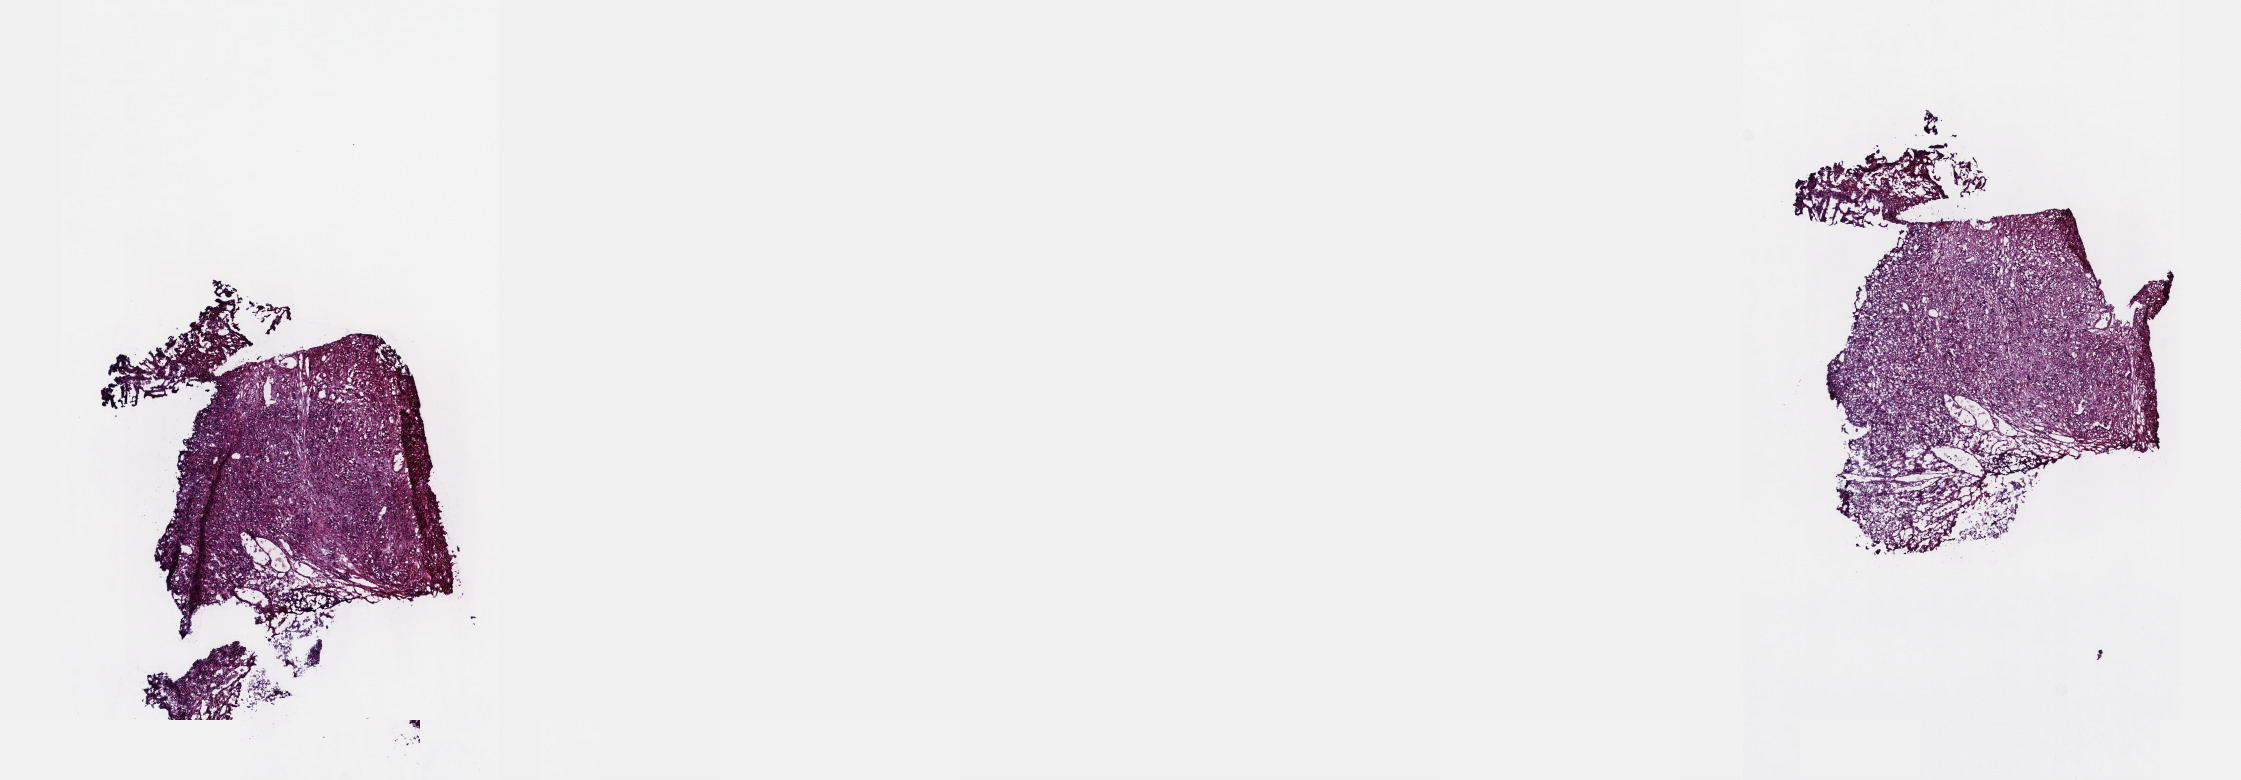
Whole-slide histology image, H&E-stained — shown as a low-resolution overview of the whole scanned area (about 18.1 x 6.3 mm, from a 40x scan), frozen section from the top of the tissue portion, sample: primary tumour, bladder. Patient: female, age at initial diagnosis 62 years. Histologic grade: high grade. Composition of this section per pathologist review: tumour cells 70%, tumour nuclei 80%, normal cells 10%, stromal cells 20%, necrosis 0%. Infiltration values recorded for this section: lymphocyte infiltration 0%, monocyte infiltration 0%, neutrophil infiltration 0%.
• AJCC pathologic stage: IV (7th edition)
• diagnosis: Transitional cell carcinoma